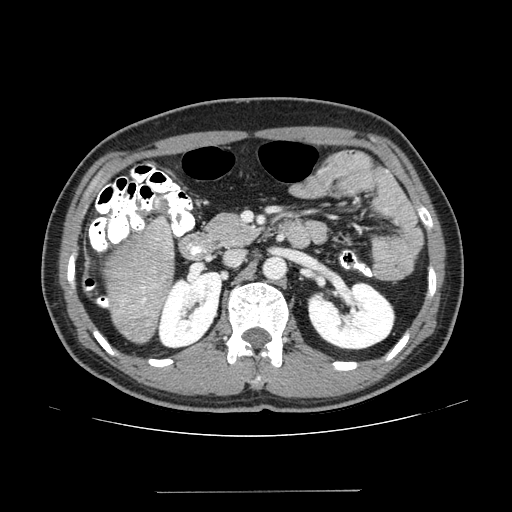
Contrast-enhanced abdominal CT (liver protocol), one axial slice; position 62 of 131 along the scan axis; one of 2 acquisitions stored at this slice position; soft-tissue window (W 400 / L 40 HU); 512 × 512 image matrix, field of view 380 × 380 mm. Case-level facts recorded for this patient, not image findings: diagnosis: hepatocellular carcinoma (patient treated with transarterial chemoembolisation; whether this scan precedes or follows treatment is not stated here); TNM stage (as recorded): Stage-I; Child-Pugh class: A; tumour differentiation: poorly differentiated.
Structures marked on this image (semi-automatic segmentation, software-assisted and operator-edited):
- liver parenchyma outside the tumour (the mass and vessels are separate outlines, so this box may not span the whole liver): bounding box <124,314,156,340> (left, top, right, bottom; pixels)